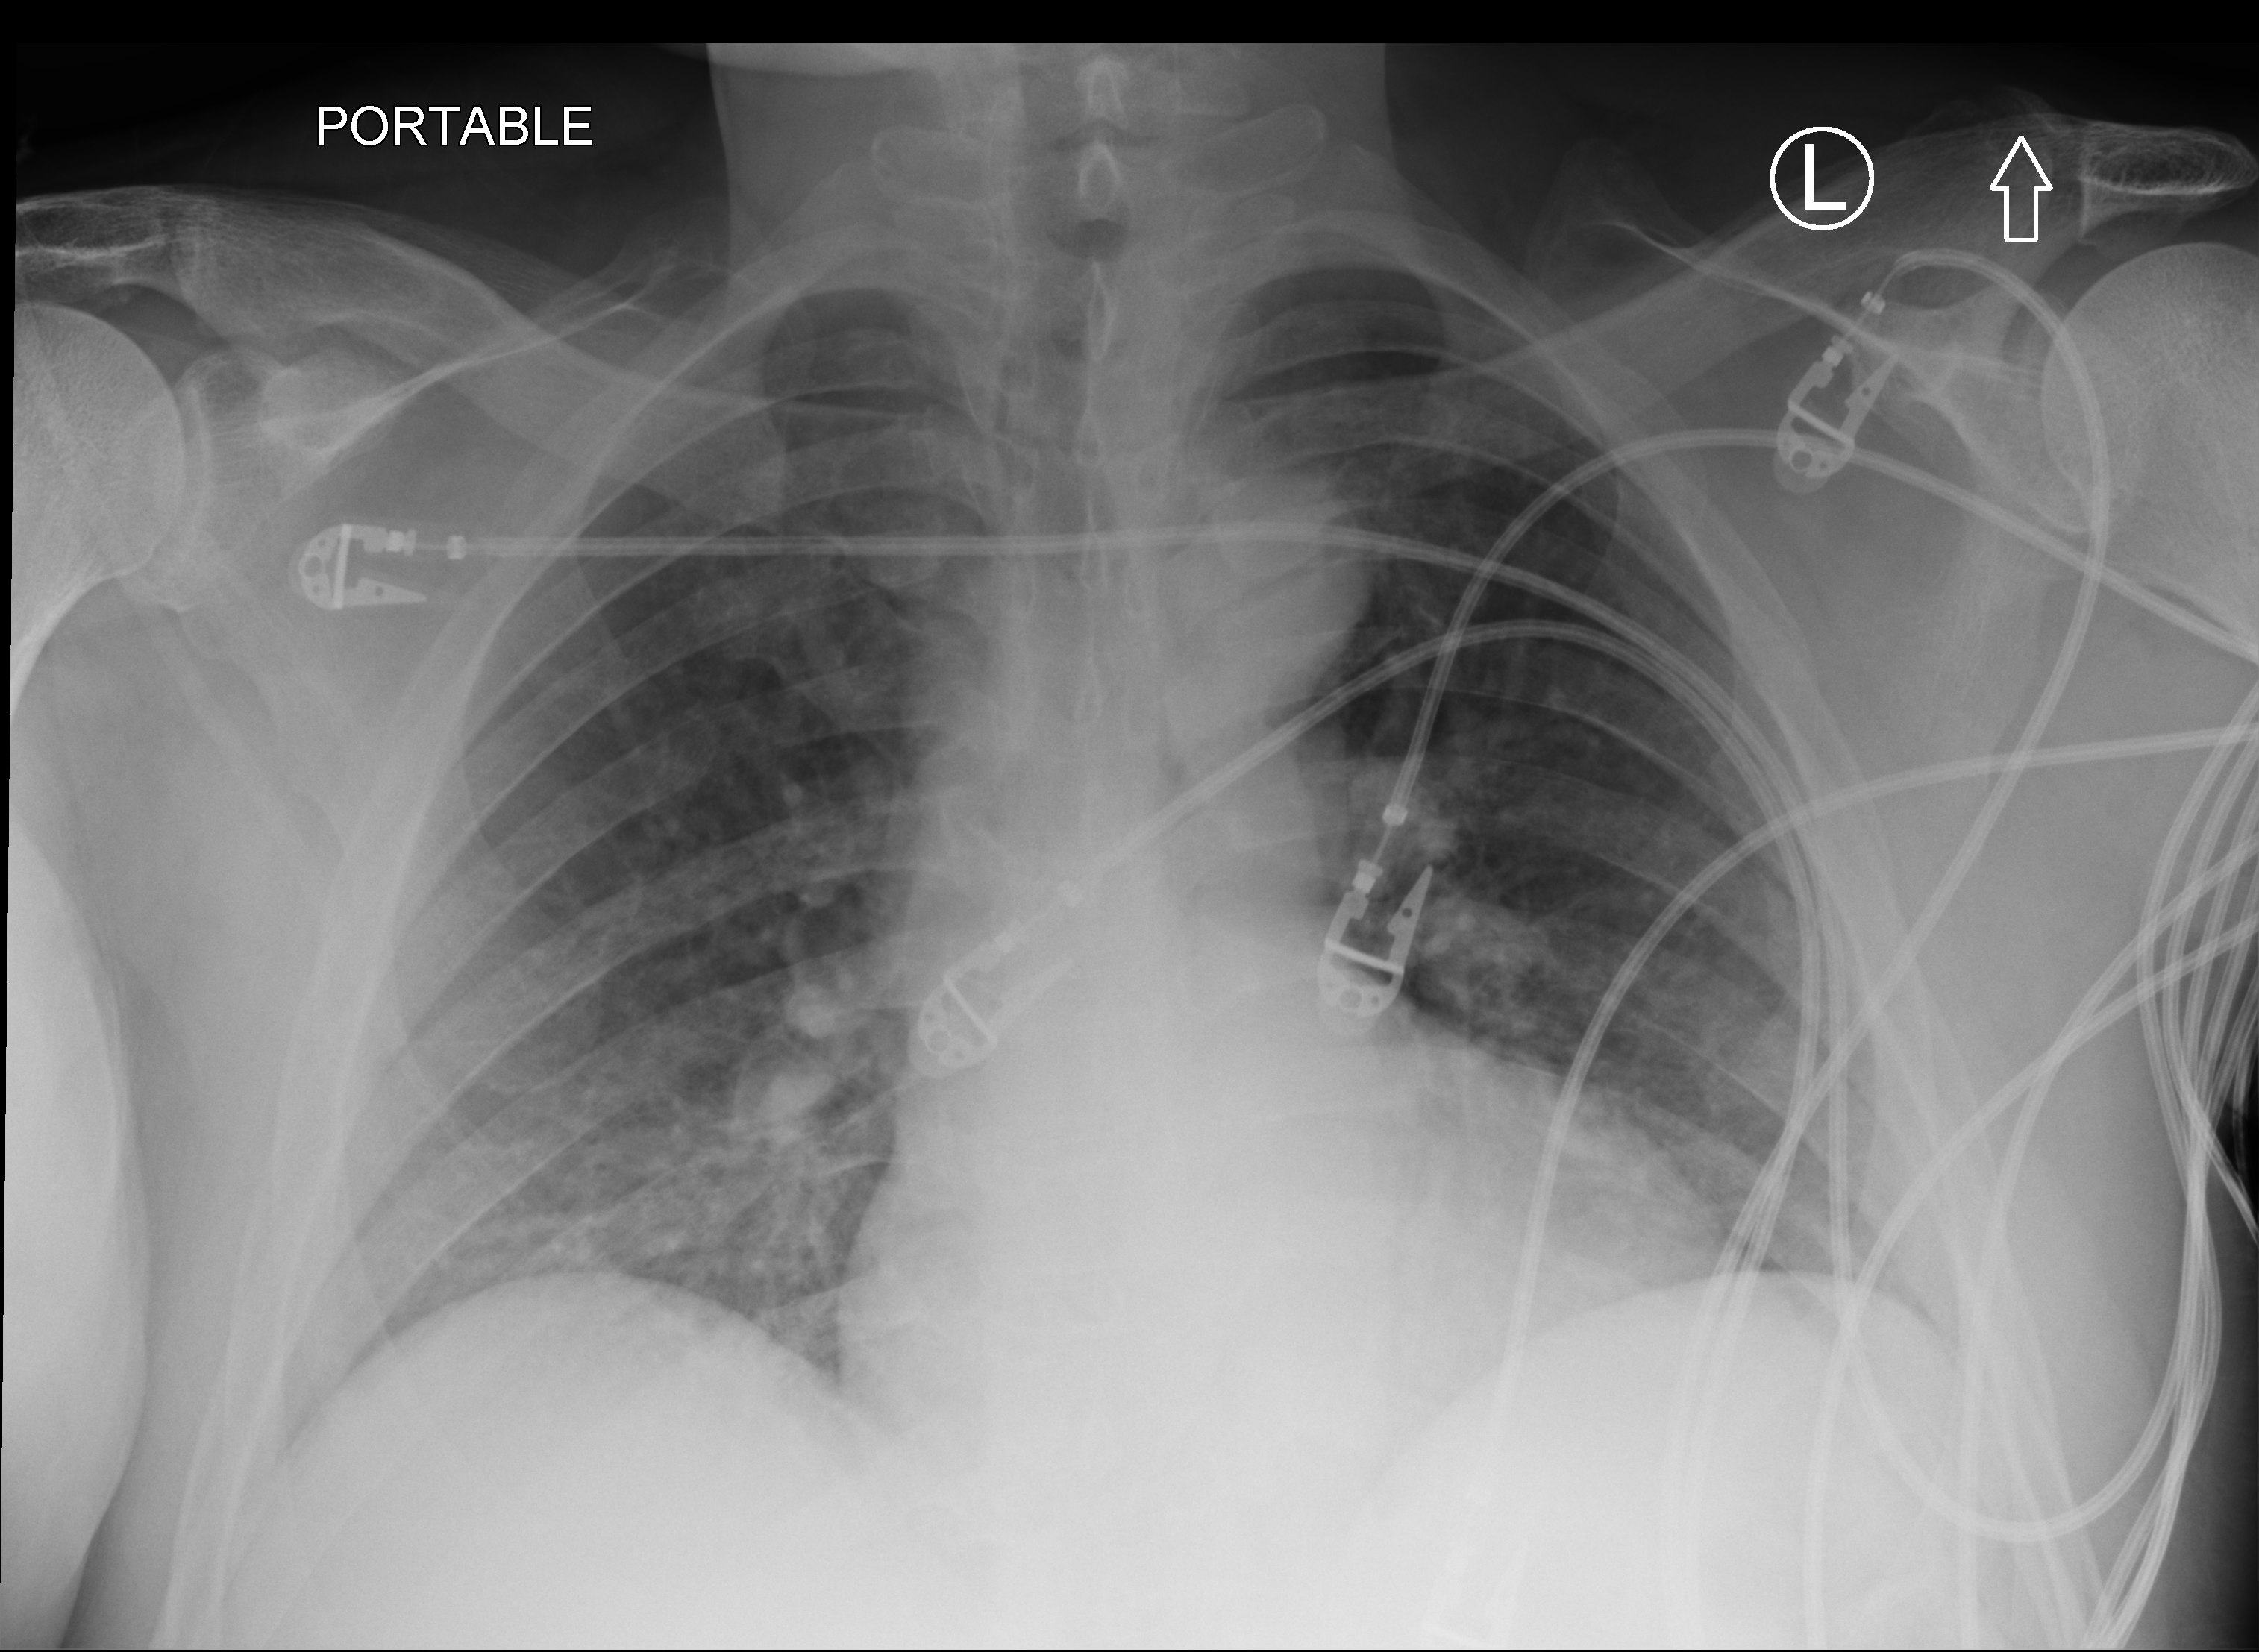
Chest X-ray (portable), anteroposterior (AP) projection. Patient hospitalised with COVID-19; male, aged 18–59 years.
Admission-level facts for this patient (not findings on this image; timing relative to this image not recorded):
- mechanically ventilated during this hospital stay: no
- admitted to intensive care during this hospital stay: no